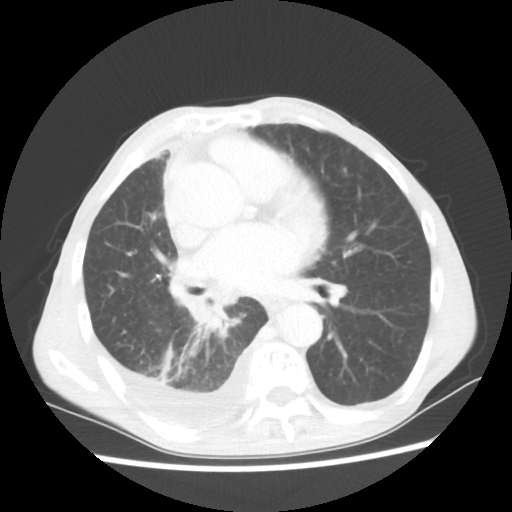
Chest CT, one axial slice; position 29 of 60 along the scan axis; lung window (W 1500 / L -600 HU); 5 mm slice thickness; 512 × 512 image matrix, field of view 335 × 335 mm. Male patient, age 76 years. From the clinical record (not read from this slice): clinical TNM (as recorded): T3 N3 M1a; histopathological grade: G3.
Annotated regions visible in this slice (rectangle marked by the reading radiologist):
- lung tumour (recorded histology: squamous cell carcinoma): bounding box (x1, y1, x2, y2) in pixels: (183, 296, 244, 350)